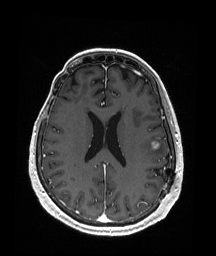
Brain MRI from a brain-tumour surgery series, one axial slice; T1-weighted post-contrast; 1 mm slice thickness; 216 × 256 image matrix. Case-level facts recorded for this patient, not image findings: histopathology: Metastatic Malignant Melanoma; tumour location: Left Frontal.
Outlined on this slice (manually delineated by an expert):
- tumour: box from (x=151, y=141) to (x=160, y=149) px